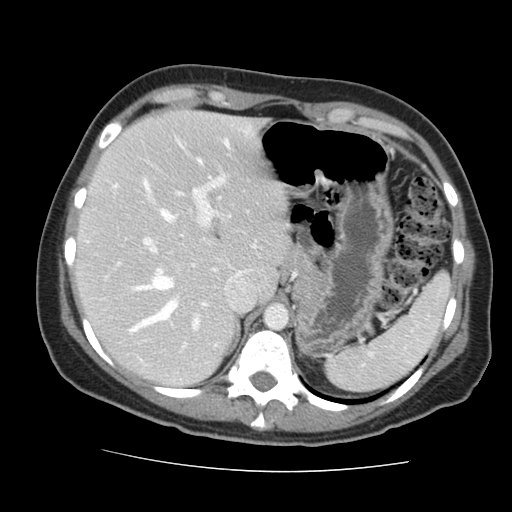
Contrast-enhanced abdominal CT, one axial slice. Position 107 of 144 along the scan axis. Soft-tissue window (W 400 / L 40 HU). 512 × 512 image matrix, field of view 333 × 333 mm. Female patient, age 46 years. From the clinical record (not read from this slice): diagnosis: colorectal cancer liver metastases, imaged before liver resection; multiple liver metastases: no; largest metastasis: 2.8 cm; disease in both lobes: no.
Structures marked on this image (manually delineated by an expert):
- hepatic veins: bounding box <113,180,178,318> (left, top, right, bottom; pixels)
- liver: <79,111,285,384>
- planned liver remnant (the part of the liver to remain after resection): <79,111,285,384>
- portal vein (with intrahepatic branches): <117,177,231,333>